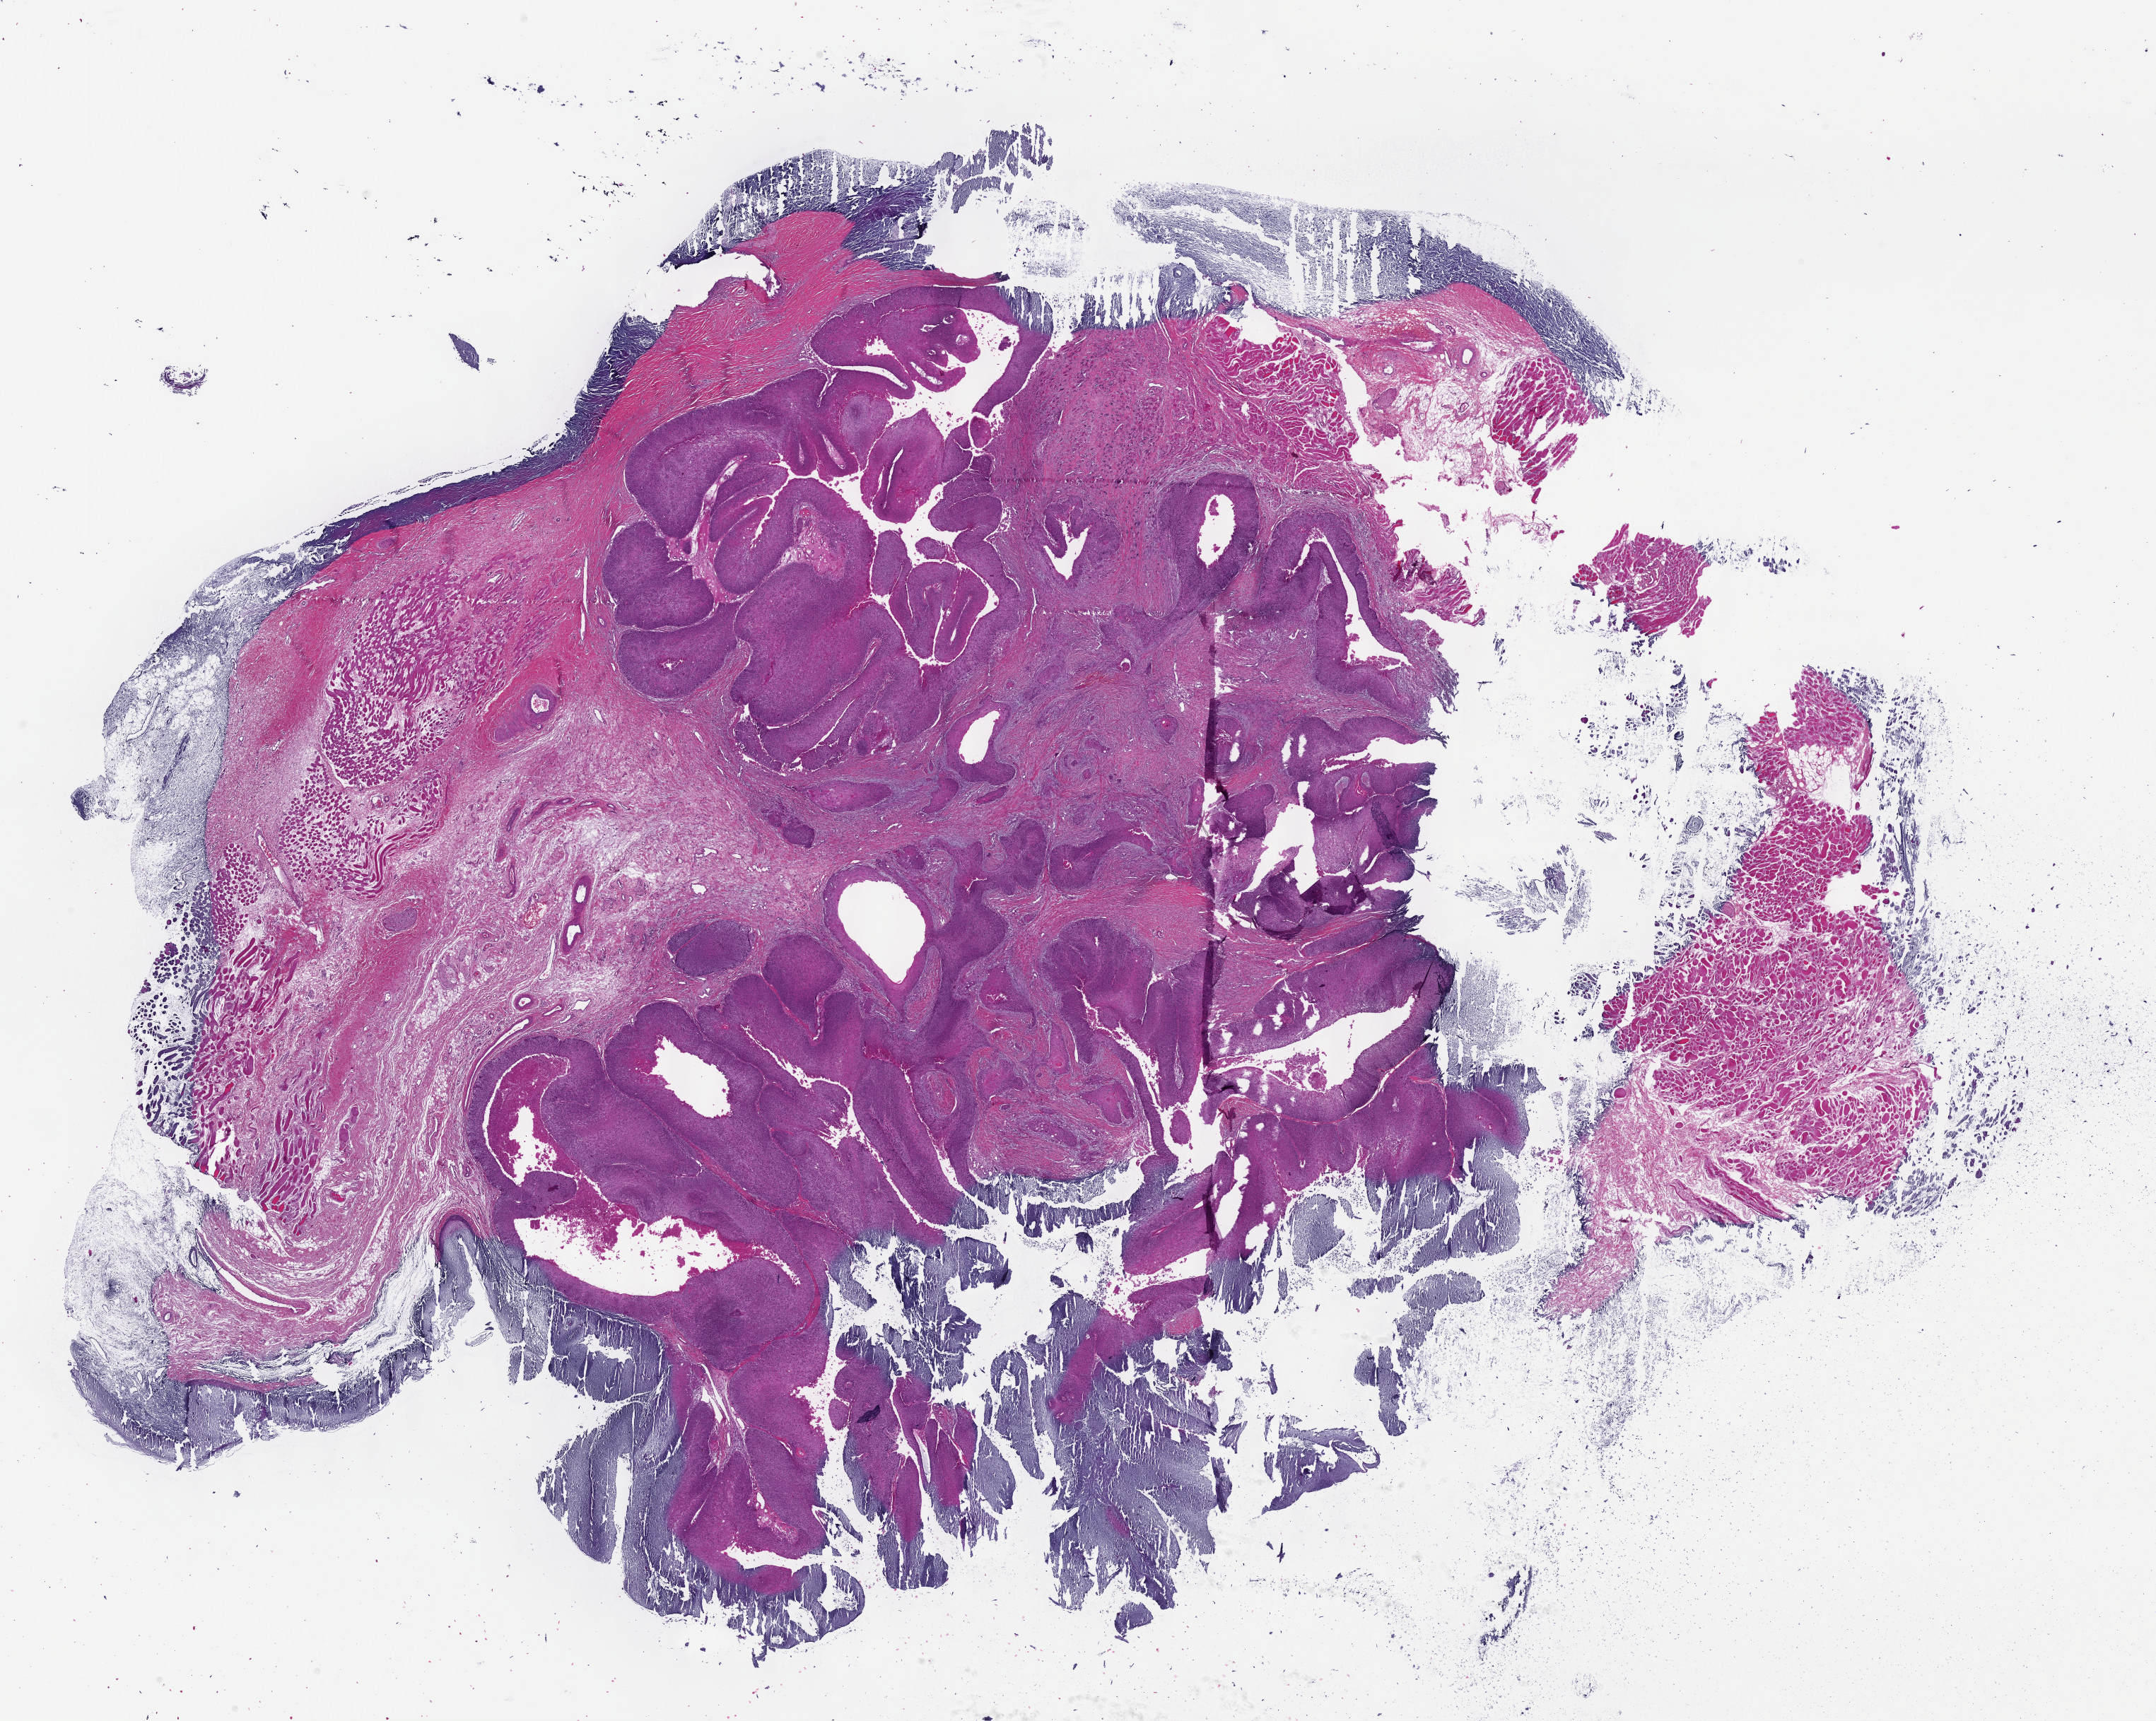
Digitized H&E-stained tissue section (whole slide) — low-resolution overview of the scanned area, about 24.6 x 19.7 mm (from a 40x scan); formalin-fixed paraffin-embedded (FFPE) diagnostic section; sample: primary tumour, head and neck. Patient: male, age at initial diagnosis 56 years. Histologic grade: G2 (moderately differentiated).
* AJCC pathologic stage: IVA (7th edition)
* diagnosis: Squamous cell carcinoma, NOS (larynx, NOS)